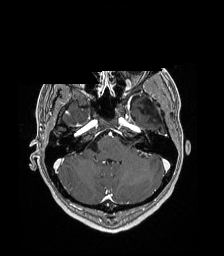
Brain MRI from a brain-tumour surgery series, one axial slice; position 136 of 192 along the scan axis; T1-weighted post-contrast; 1 mm slice thickness; 224 × 256 image matrix, field of view 224 × 256 mm. Case-level facts recorded for this patient, not image findings: histopathology: Low grade glioma; IDH mutation: no.
Annotated regions visible in this slice (outlined manually by an expert reader):
- previous resection cavity: bounding box [x1, y1, x2, y2] px = [147, 110, 150, 113]